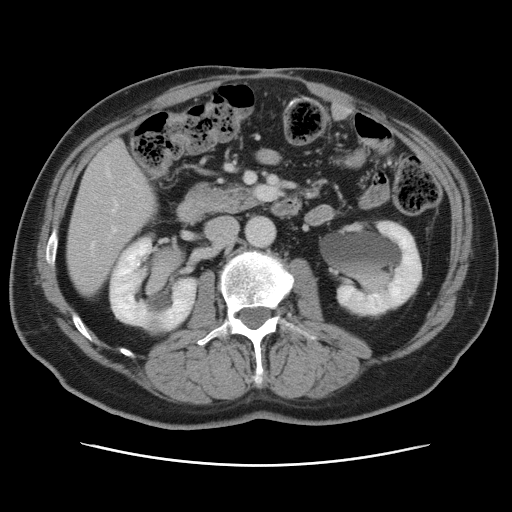
Contrast-enhanced abdominal CT, one axial slice. Slice 27 of 80 in the series (ordered by position). 120 kVp. Intravenous contrast given. Soft-tissue window (W 400 / L 40 HU). 5 mm slice thickness. 512 × 512 image matrix. Male patient, age 69 years. From the clinical record (not read from this slice): diagnosis: colorectal cancer liver metastases, imaged before liver resection; multiple liver metastases: no; largest metastasis: 5 cm; disease in both lobes: yes.
Annotated regions visible in this slice (expert manual segmentation):
- hepatic veins: box from (x=90, y=170) to (x=117, y=248) px
- liver: (x=68, y=142)–(x=156, y=294)
- planned liver remnant (the part of the liver to remain after resection): (x=68, y=218)–(x=133, y=294)